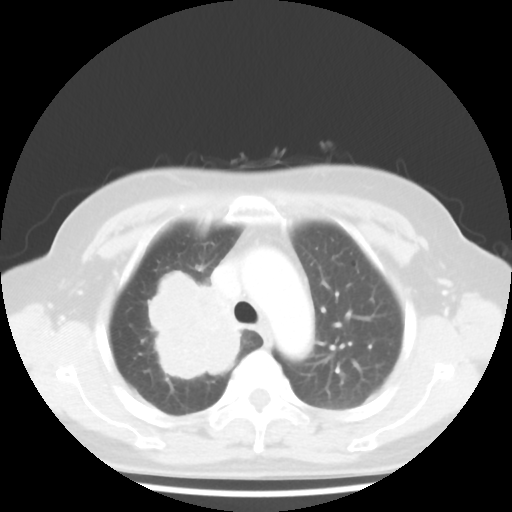
Chest CT, one axial slice. Position 33 of 44 along the scan axis. Reconstruction kernel STANDARD. 100 kVp. Lung window (W 1500 / L -600 HU). 512 × 512 image matrix, field of view 316 × 316 mm. Female patient, age 62 years. From the clinical record (not read from this slice): clinical TNM (as recorded): T3 N0 M0; histopathological grade: G3.
Outlined on this slice (bounding box drawn by a radiologist):
- lung tumour (recorded histology: small cell carcinoma): bounding box <137,258,249,398> (left, top, right, bottom; pixels)